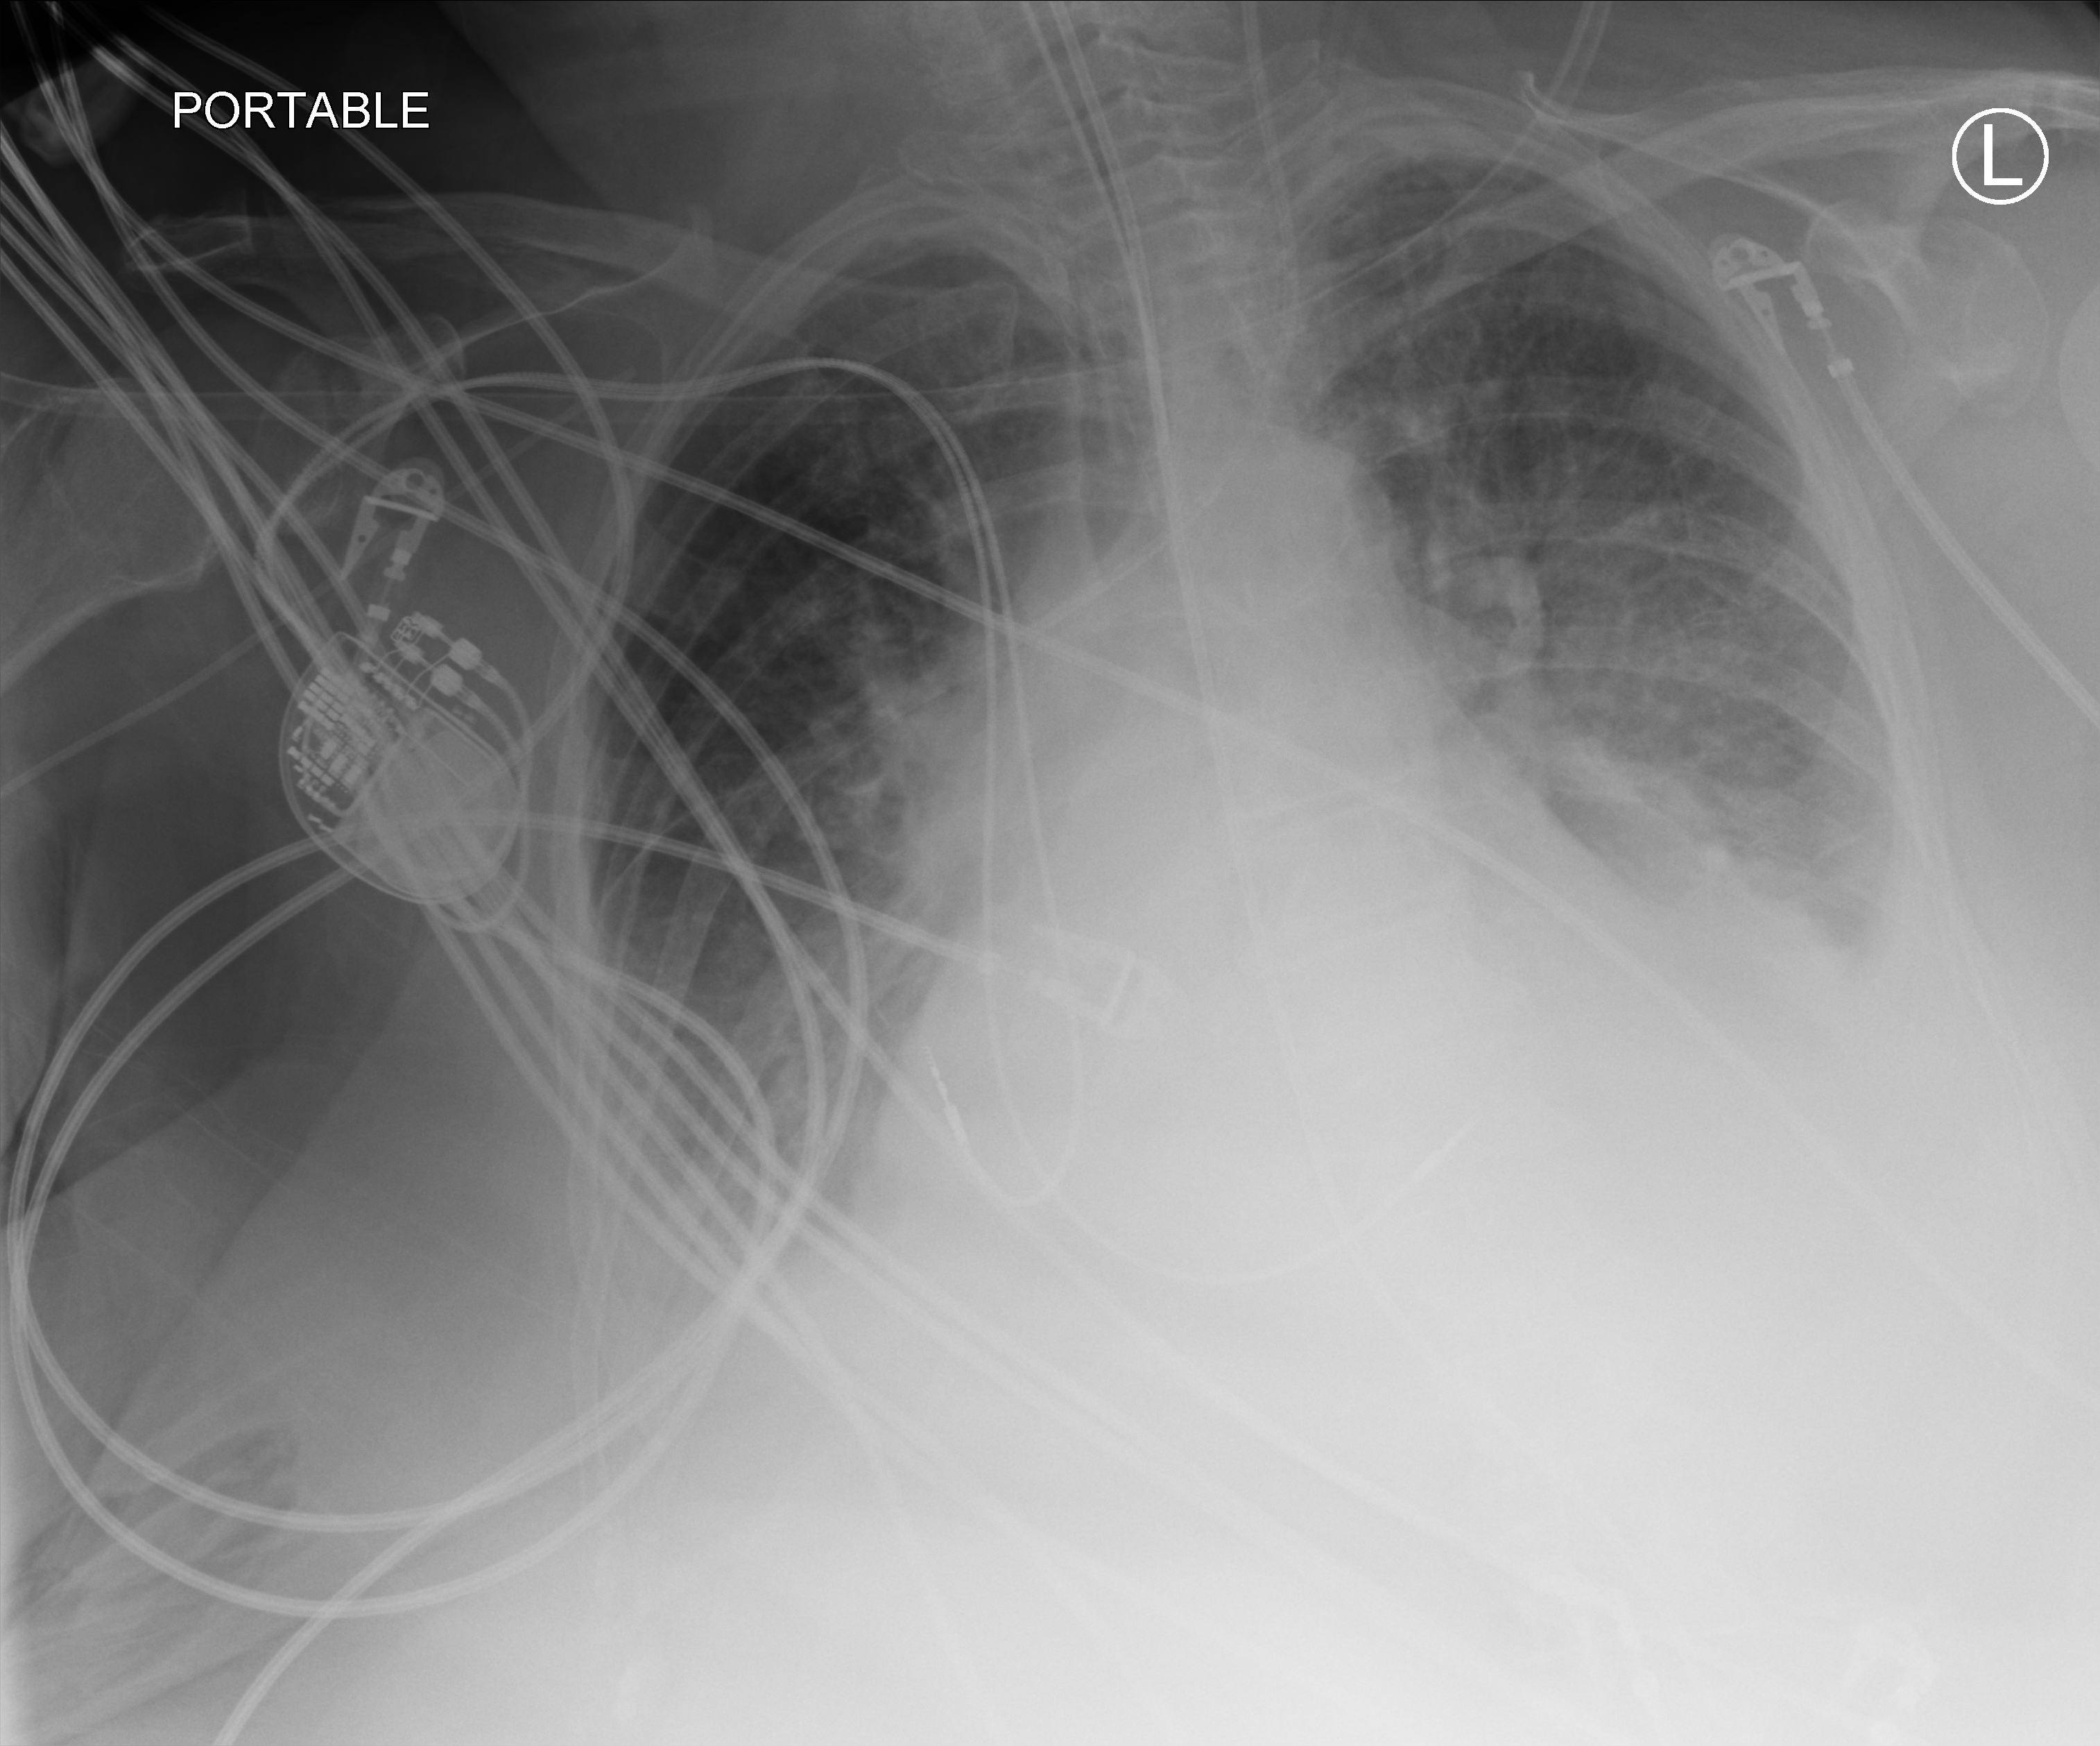
Bedside chest radiograph (computed radiography), anteroposterior (AP) projection. Patient hospitalised with COVID-19; female, aged 75–90 years.
Admission-level facts for this patient (not findings on this image; timing relative to this image not recorded): admitted to intensive care during this hospital stay: yes.